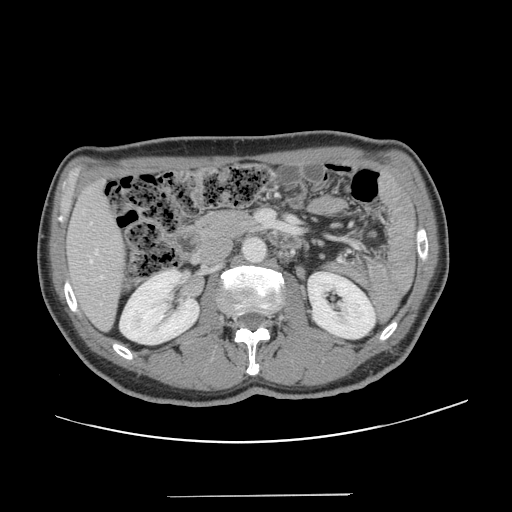
Contrast-enhanced abdominal CT, one axial slice; position 59 of 131 along the scan axis; 120 kVp; soft-tissue window (W 400 / L 40 HU); 2.5 mm slice thickness; 512 × 512 image matrix. Male patient, age 60 years. Case-level facts recorded for this patient, not image findings: diagnosis: colorectal cancer liver metastases, imaged before liver resection; multiple liver metastases: no; largest metastasis: 2.5 cm; disease in both lobes: no.
Annotated regions visible in this slice (outlined manually by an expert reader):
- hepatic veins: bounding box [x1, y1, x2, y2] px = [90, 250, 98, 263]
- liver: [68, 184, 123, 328]
- planned liver remnant (the part of the liver to remain after resection): [68, 184, 124, 329]